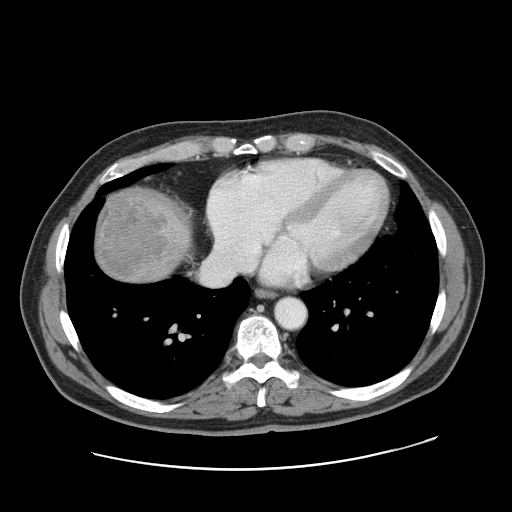
Contrast-enhanced abdominal CT, one axial slice. Position 157 of 178 along the scan axis. 120 kVp. Intravenous contrast given. Soft-tissue window (W 400 / L 40 HU). 2.5 mm slice thickness. 512 × 512 image matrix, field of view 403 × 403 mm. Male patient, age 63 years. From the clinical record (not read from this slice): diagnosis: colorectal cancer liver metastases, imaged before liver resection; multiple liver metastases: yes; largest metastasis: 8 cm; disease in both lobes: yes.
Outlined on this slice (manually delineated by an expert):
- liver: bounding box <93,189,193,284> (left, top, right, bottom; pixels)
- liver metastasis: <97,191,165,279>